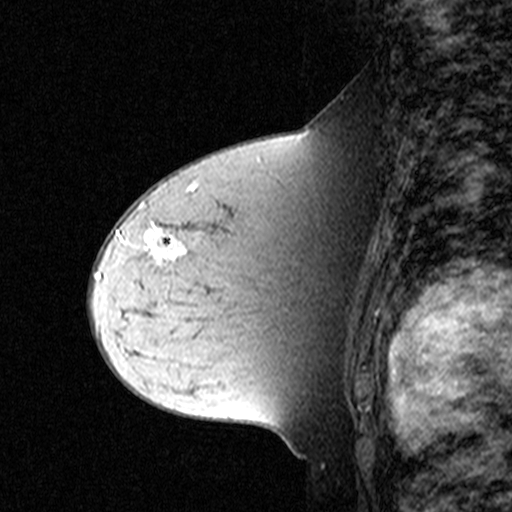
Breast MRI (dynamic contrast-enhanced), one sagittal slice. Position 26 of 44 along the scan axis. Dynamic contrast-enhanced study with each time point stored as its own series, time point 2 of 3 at this slice position (early post-contrast, ordered by acquisition time). 1.5 T. TE 4.5 ms, TR 11 ms. 3 mm slice thickness. 512 × 512 image matrix, field of view 200 × 200 mm. Female patient, age 44 years. From the clinical record (not read from this slice): setting: breast cancer imaged before/during neoadjuvant chemotherapy; receptor status: triple-negative.
Structures marked on this image (semi-automatic segmentation, software-assisted and operator-edited):
- analysis volume of interest (the breast-tissue region the enhancement analysis was run in; not a lesion): bounding box [x1, y1, x2, y2] px = [132, 212, 309, 331]
- tumour enhancement mask (voxels above the 90 % enhancement threshold inside the analysis volume of interest): [148, 228, 188, 260]